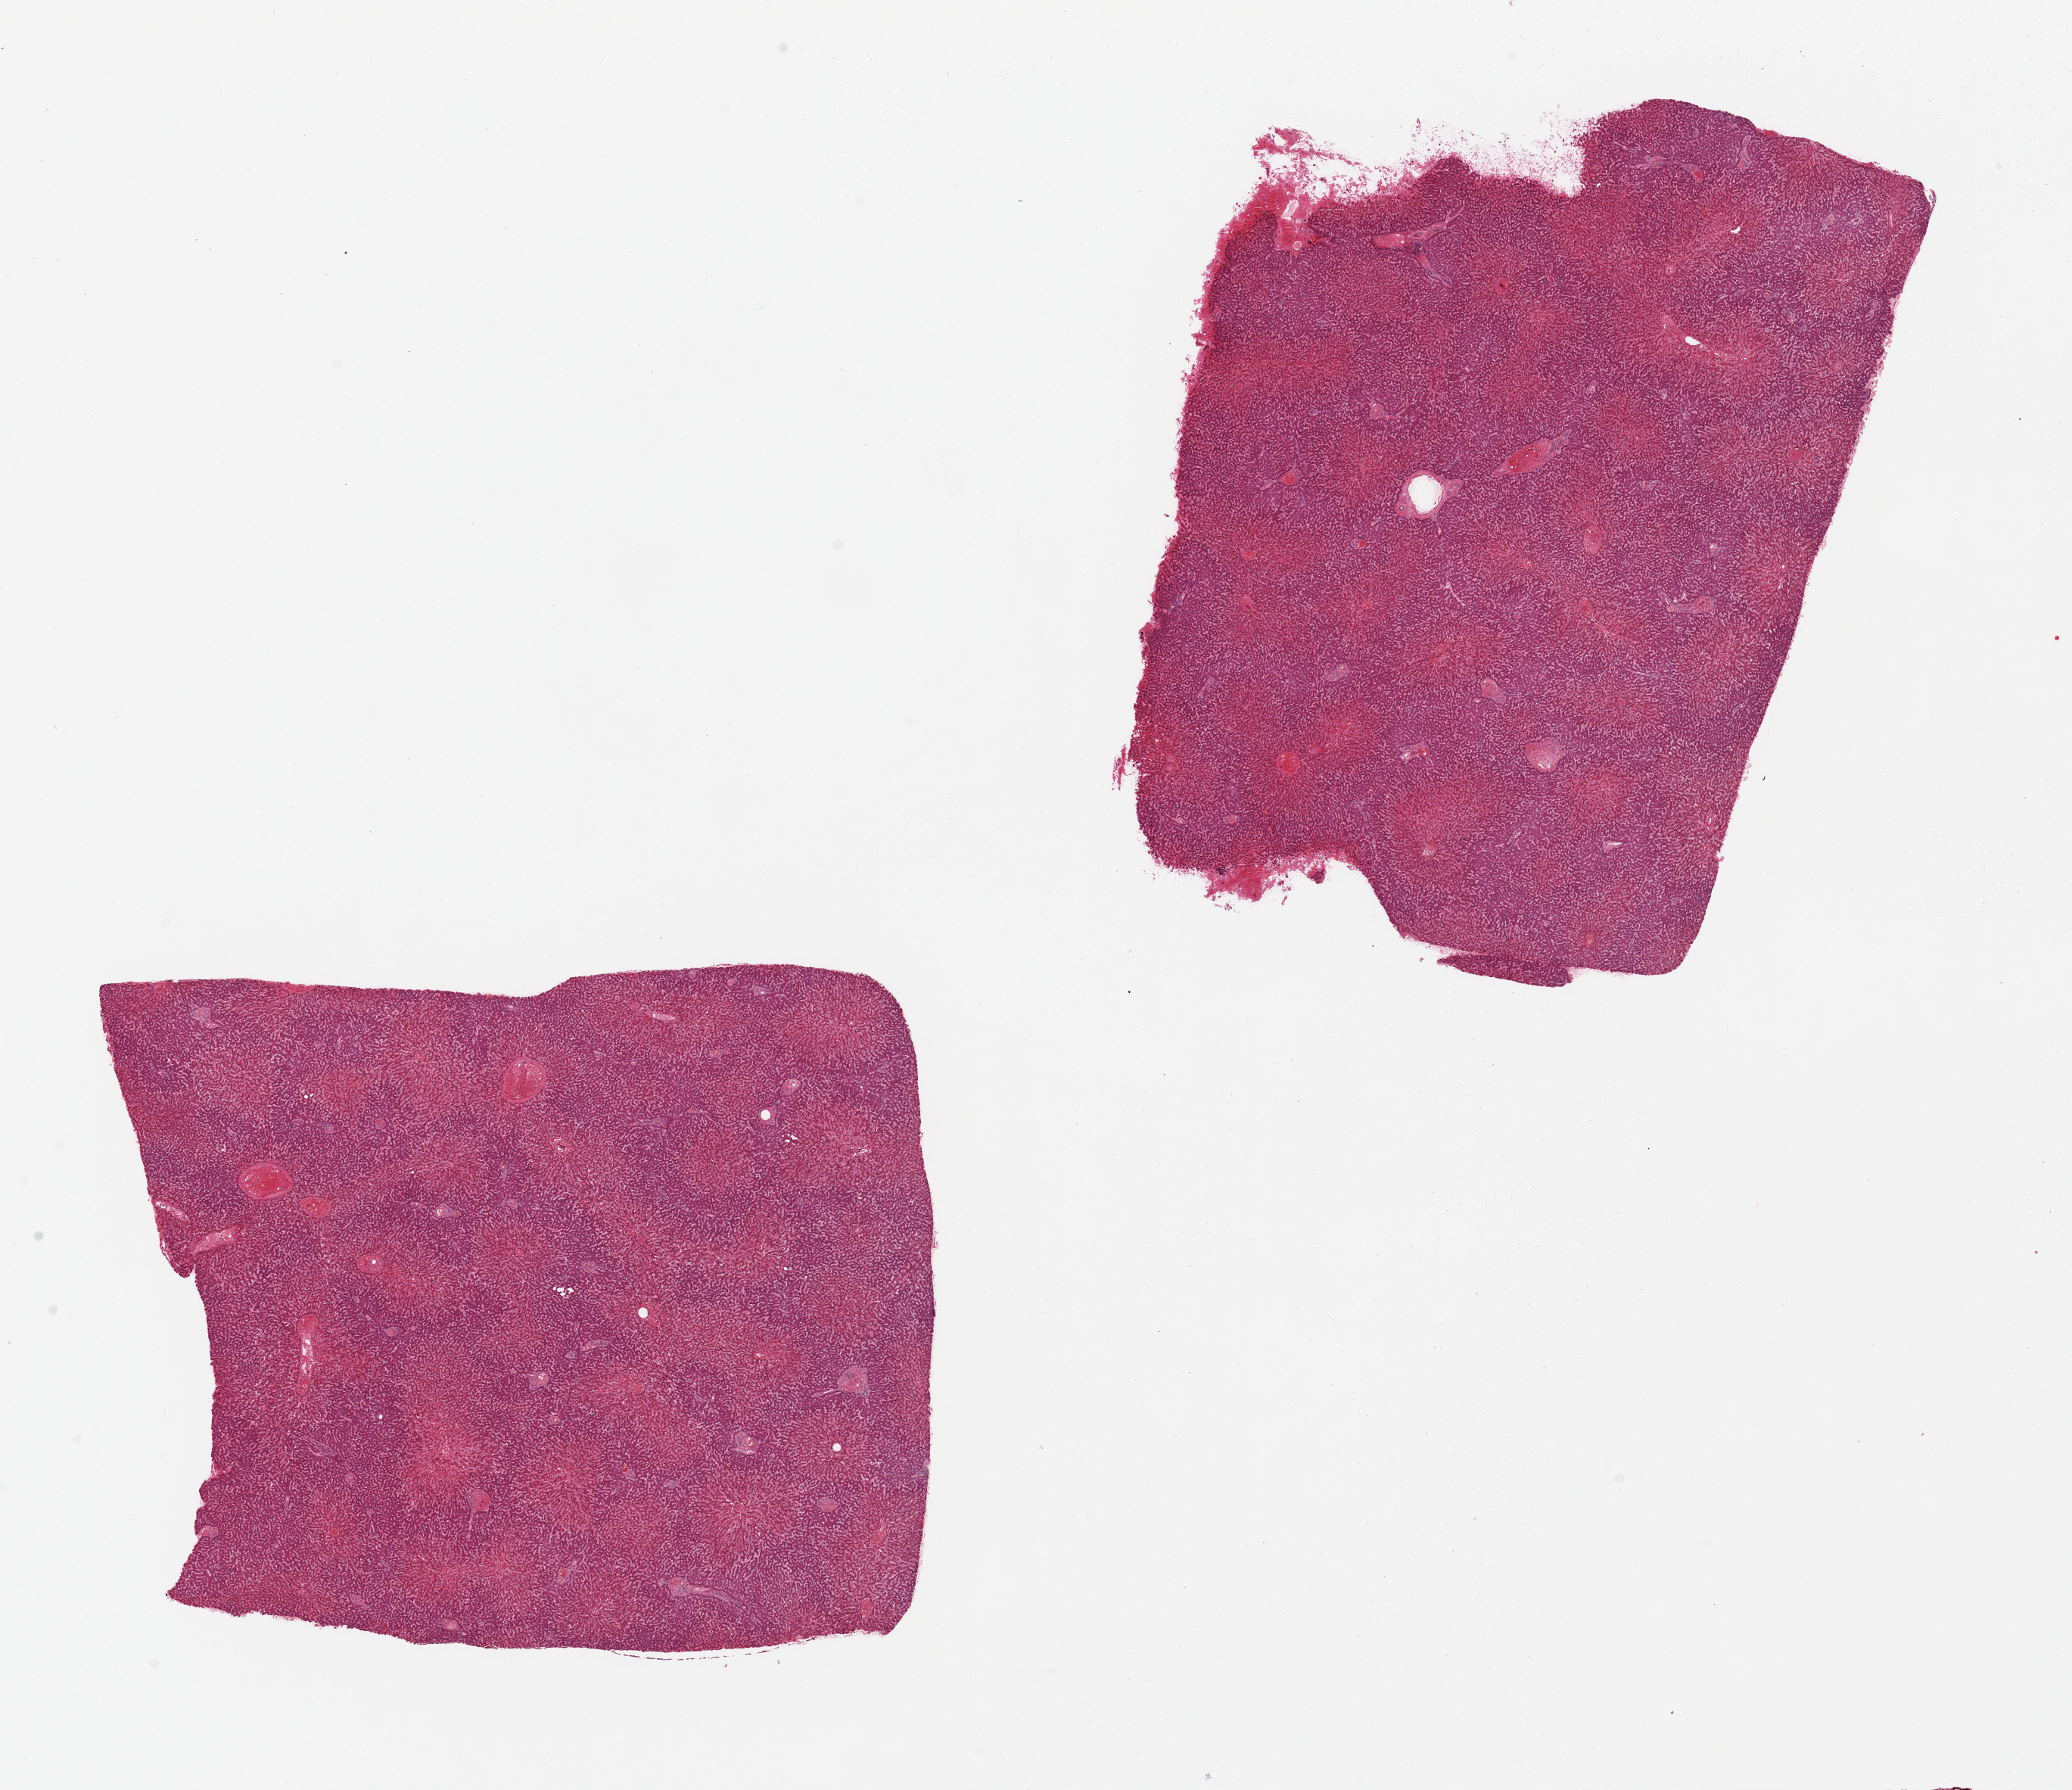
Whole-slide image, hematoxylin and eosin (H&E) stain — shown as a low-resolution overview of the whole scanned area (about 21.7 x 18.7 mm), PAXgene-fixed, paraffin-embedded tissue, target tissue: liver, donor tissue sample. Donor: female.
* reviewer comment on this tissue sample: 2 pieces, well preserved, moderate congestion, minimal steatosis